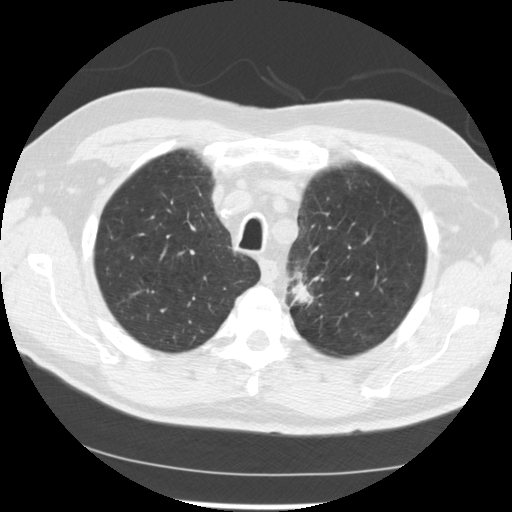
Low-dose screening chest CT, one axial slice. Slice 199 of 249 in the series (ordered by position). Lung window (W 1500 / L -600 HU). 512 × 512 image matrix, field of view 341 × 341 mm.
Outlined on this slice (expert manual segmentation):
- lesion 2 (tumor, upper lobe of left lung): bounding box [x1, y1, x2, y2] px = [291, 281, 314, 304]